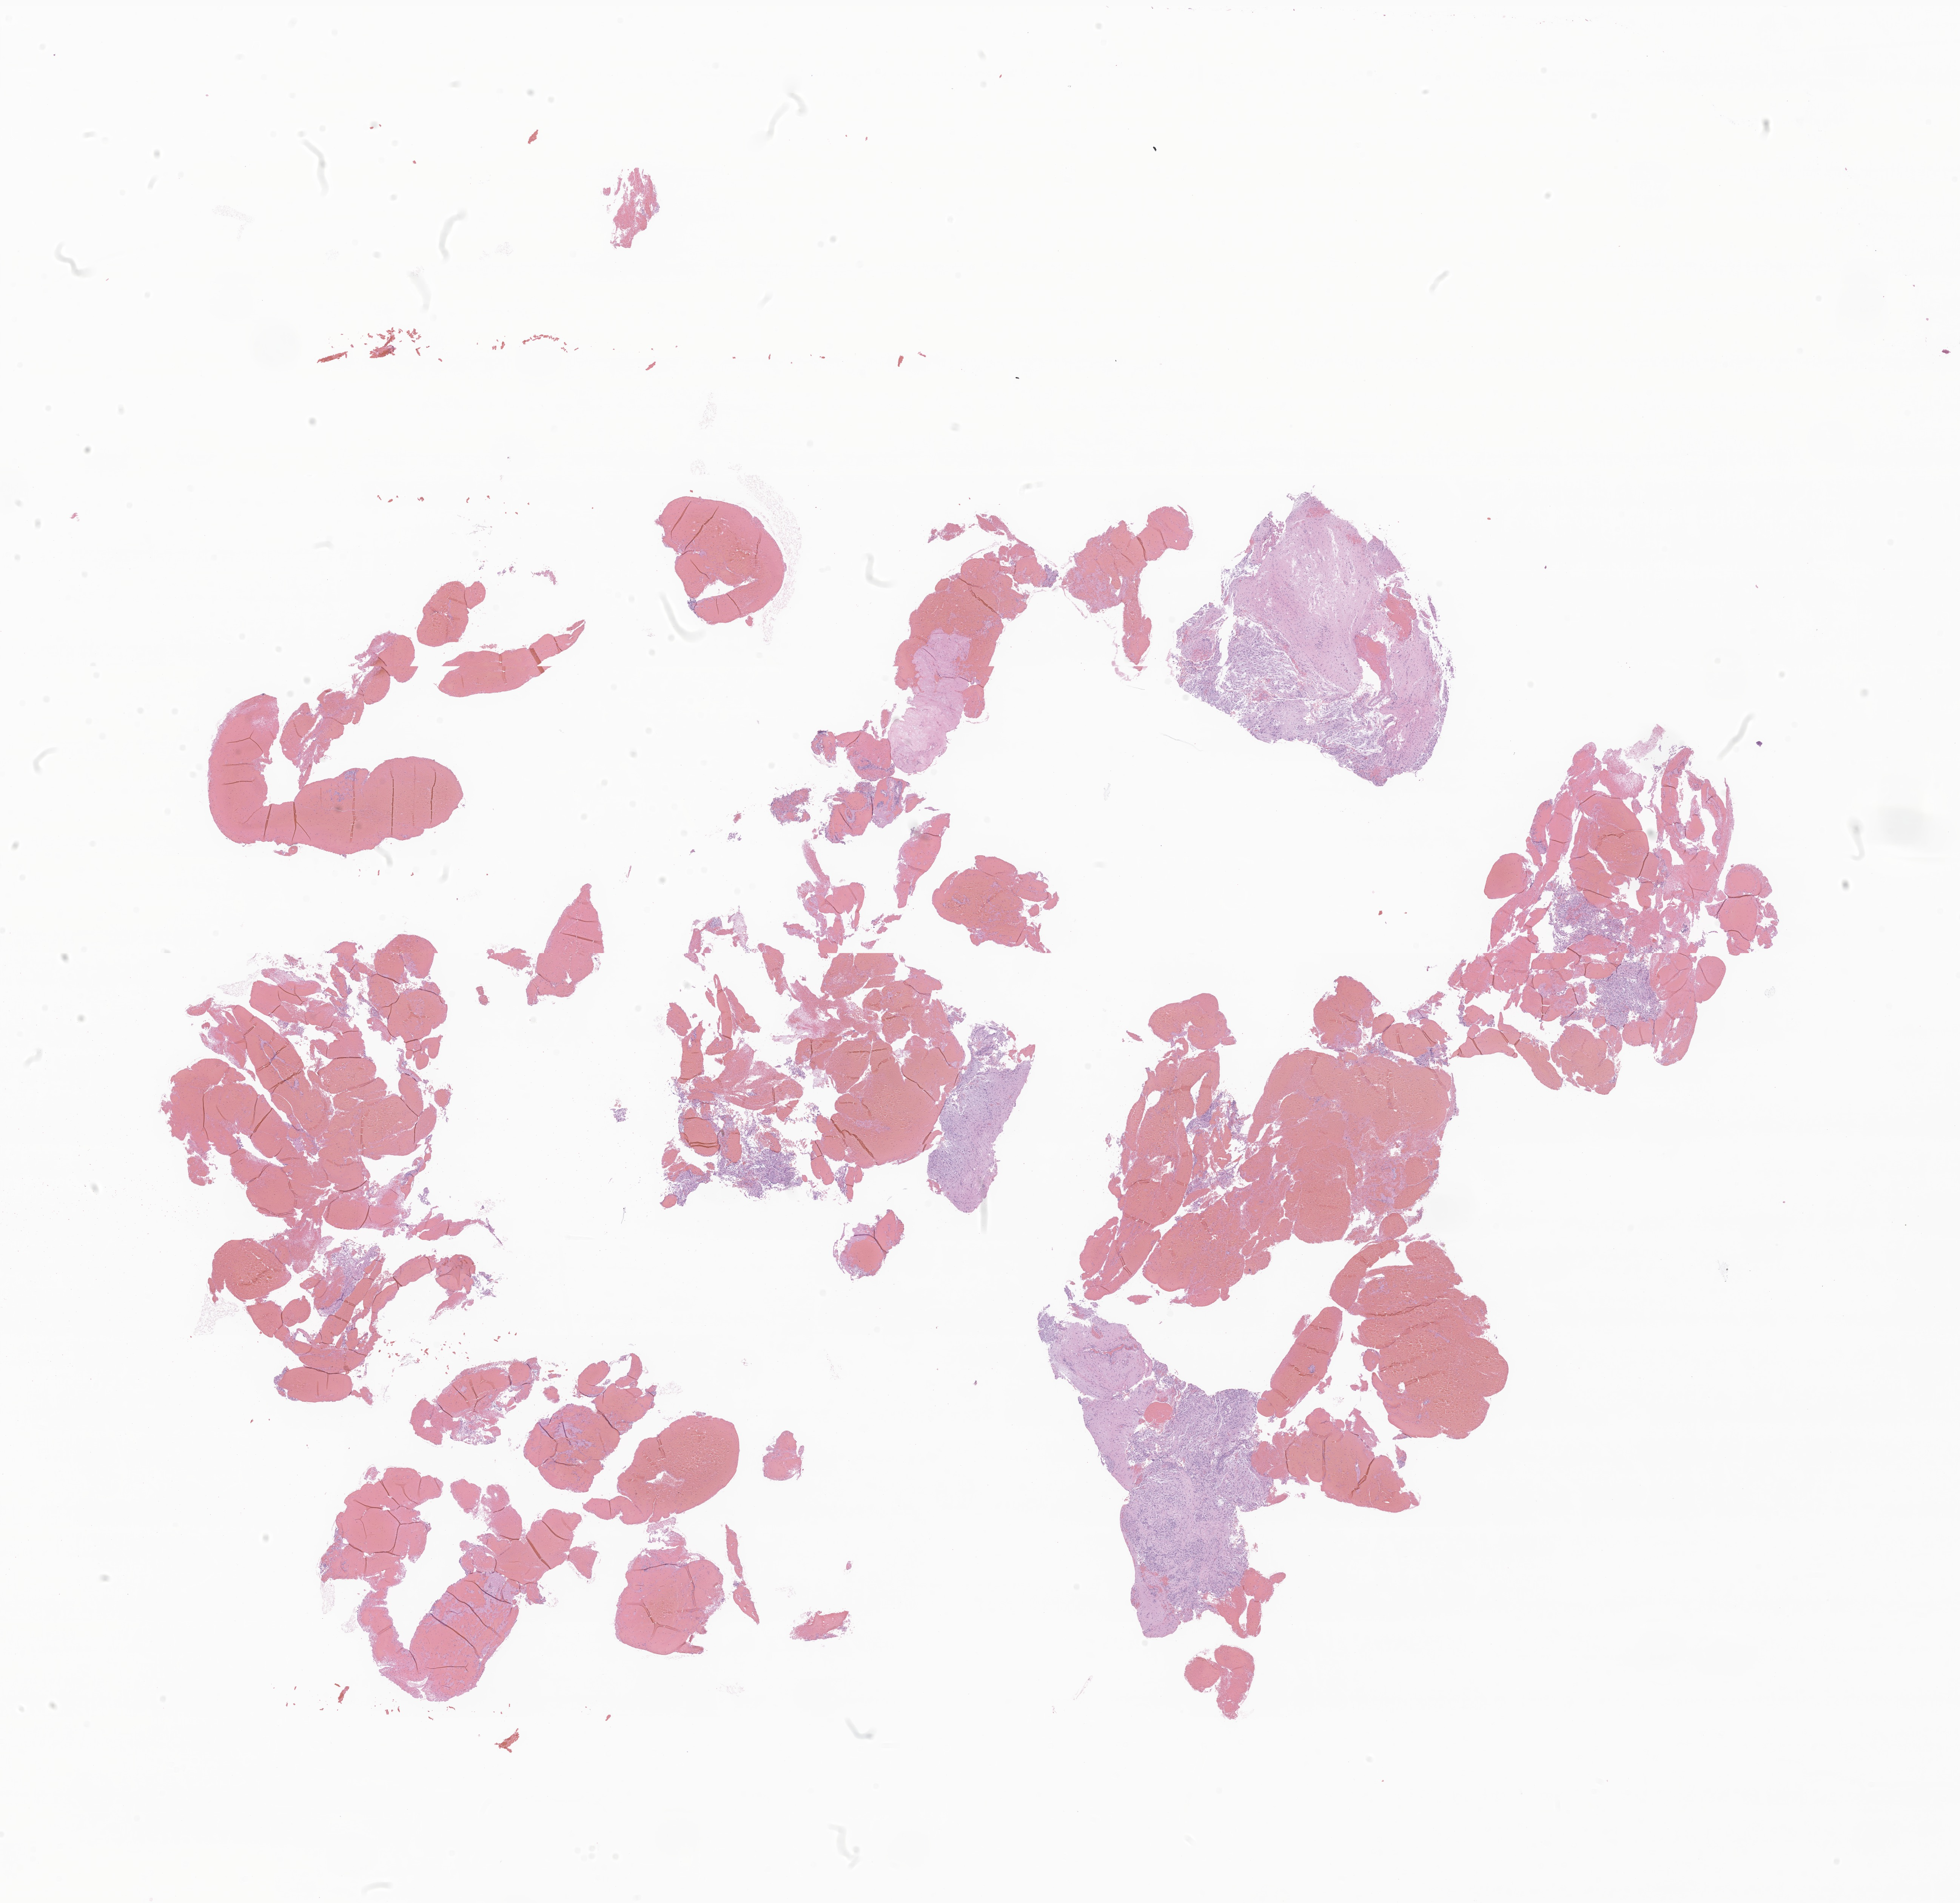
H&E whole-slide image of tumor tissue from the brain — a low-resolution overview of the entire scanned area, about 21.9 x 21.2 mm, formalin-fixed paraffin-embedded section. Patient female; age 93 months (7 years 9 months).
Recorded diagnosis: Neoplasm, uncertain whether benign or malignant.